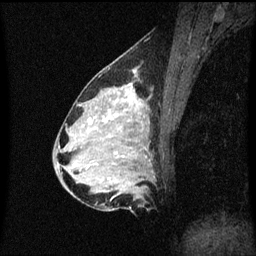
Breast MRI (dynamic contrast-enhanced), one sagittal slice; position 26 of 60 along the scan axis; dynamic contrast-enhanced series, image 2 of 3 at this slice position (ordered by acquisition); 1.5 T; TE 4.2 ms, TR 8.4 ms; 2 mm slice thickness; 256 × 256 image matrix, field of view 200 × 200 mm. Female patient, age 34 years. From the clinical record (not read from this slice): setting: breast cancer imaged before/during neoadjuvant chemotherapy; receptor status: HR-positive, HER2-negative.
Outlined on this slice (semi-automatically segmented with operator editing):
- analysis volume of interest (the breast-tissue region the enhancement analysis was run in; not a lesion): box from (x=69, y=70) to (x=154, y=209) px
- tumour enhancement mask (voxels above the 70 % enhancement threshold inside the analysis volume of interest): (x=109, y=72)–(x=142, y=119)